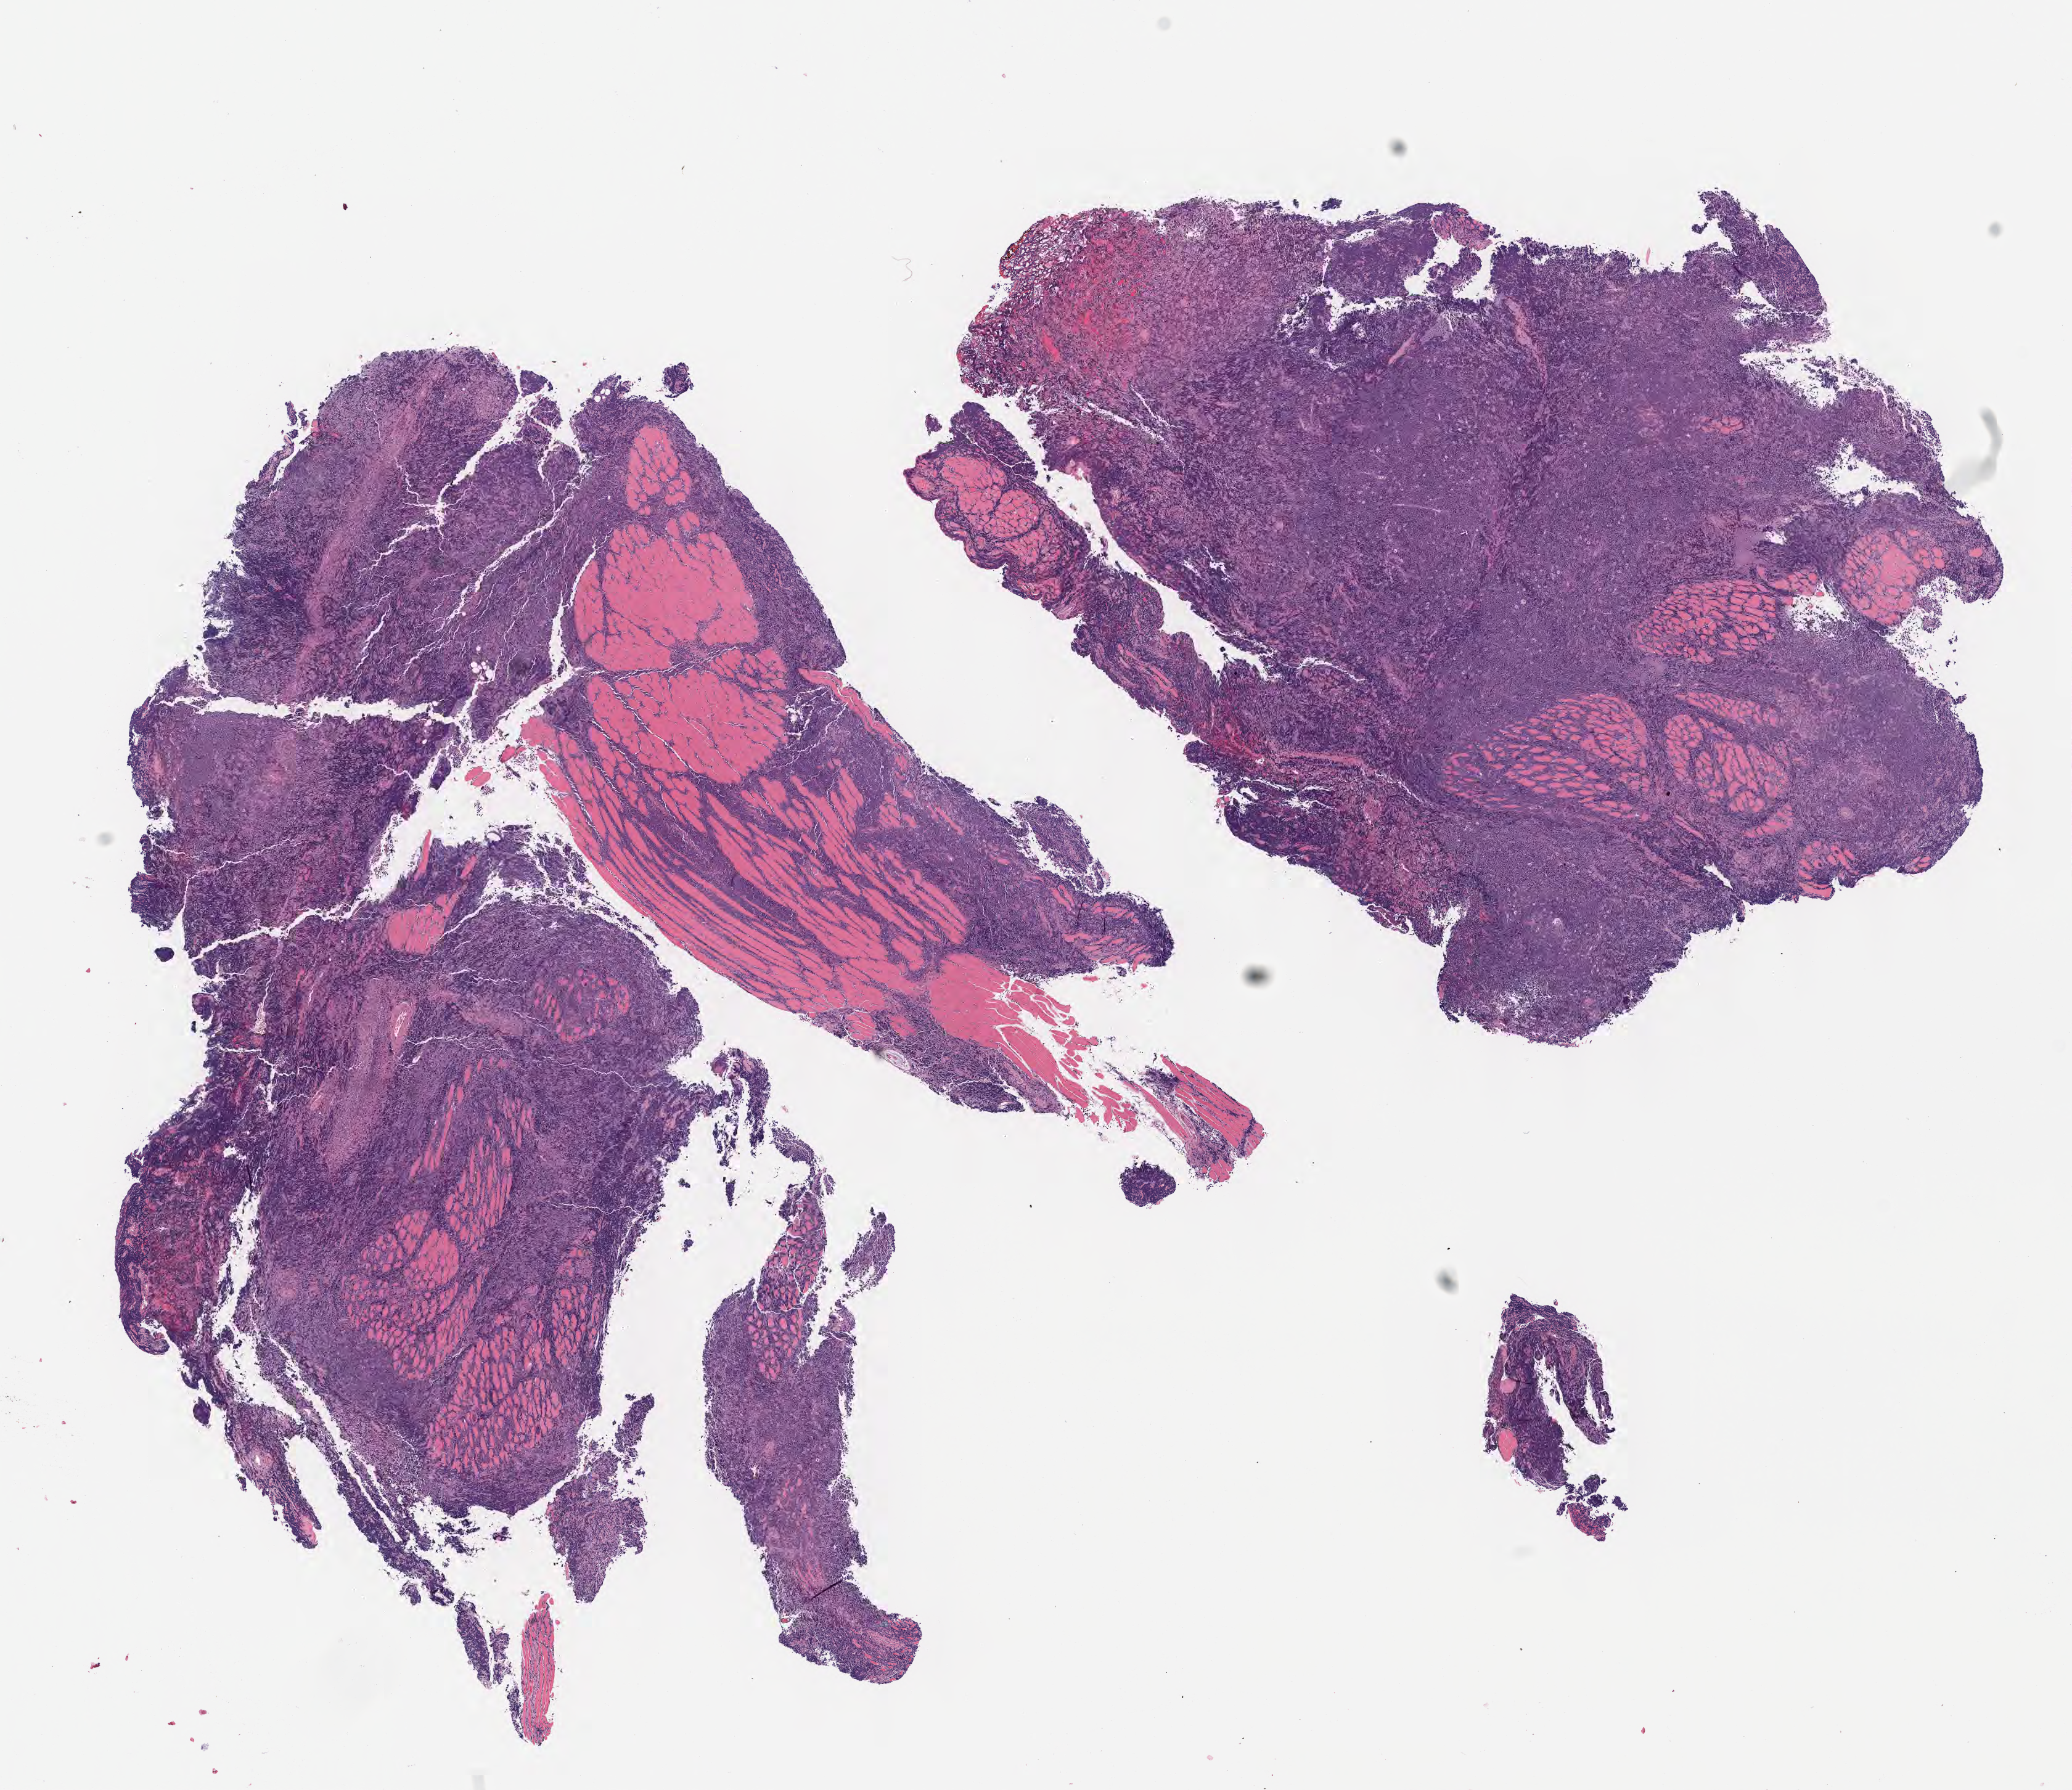
Hematoxylin and eosin (H&E) whole-slide image, low-resolution overview of the scanned area, about 13.6 x 11.7 mm; tumor tissue; site: pelvis. Male, age 7 years at initial diagnosis.
• histologic diagnosis: Diffuse large B-cell lymphoma, NOS